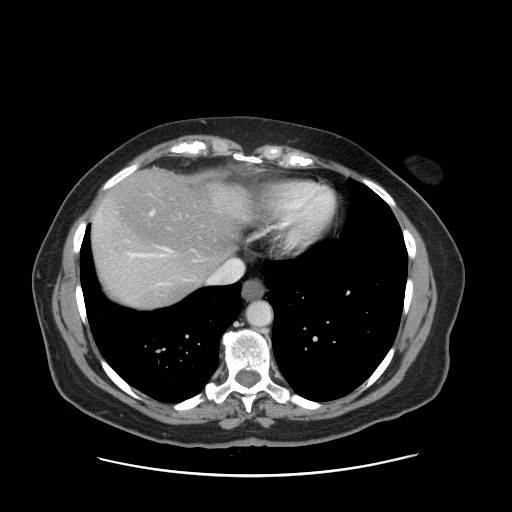
Contrast-enhanced abdominal CT, one axial slice; slice 136 of 161 in the series (ordered by position); 120 kVp; intravenous contrast given; soft-tissue window (W 400 / L 40 HU); 2.5 mm slice thickness; 512 × 512 image matrix, field of view 398 × 398 mm. Female patient, age 62 years. Case-level facts recorded for this patient, not image findings: diagnosis: colorectal cancer liver metastases, imaged before liver resection; multiple liver metastases: no; largest metastasis: 2.5 cm; disease in both lobes: no.
Structures marked on this image (expert manual segmentation):
- hepatic veins: bounding box <127,191,243,285> (left, top, right, bottom; pixels)
- liver: <93,171,252,308>
- planned liver remnant (the part of the liver to remain after resection): <96,171,251,276>
- portal vein (with intrahepatic branches): <151,211,156,215>